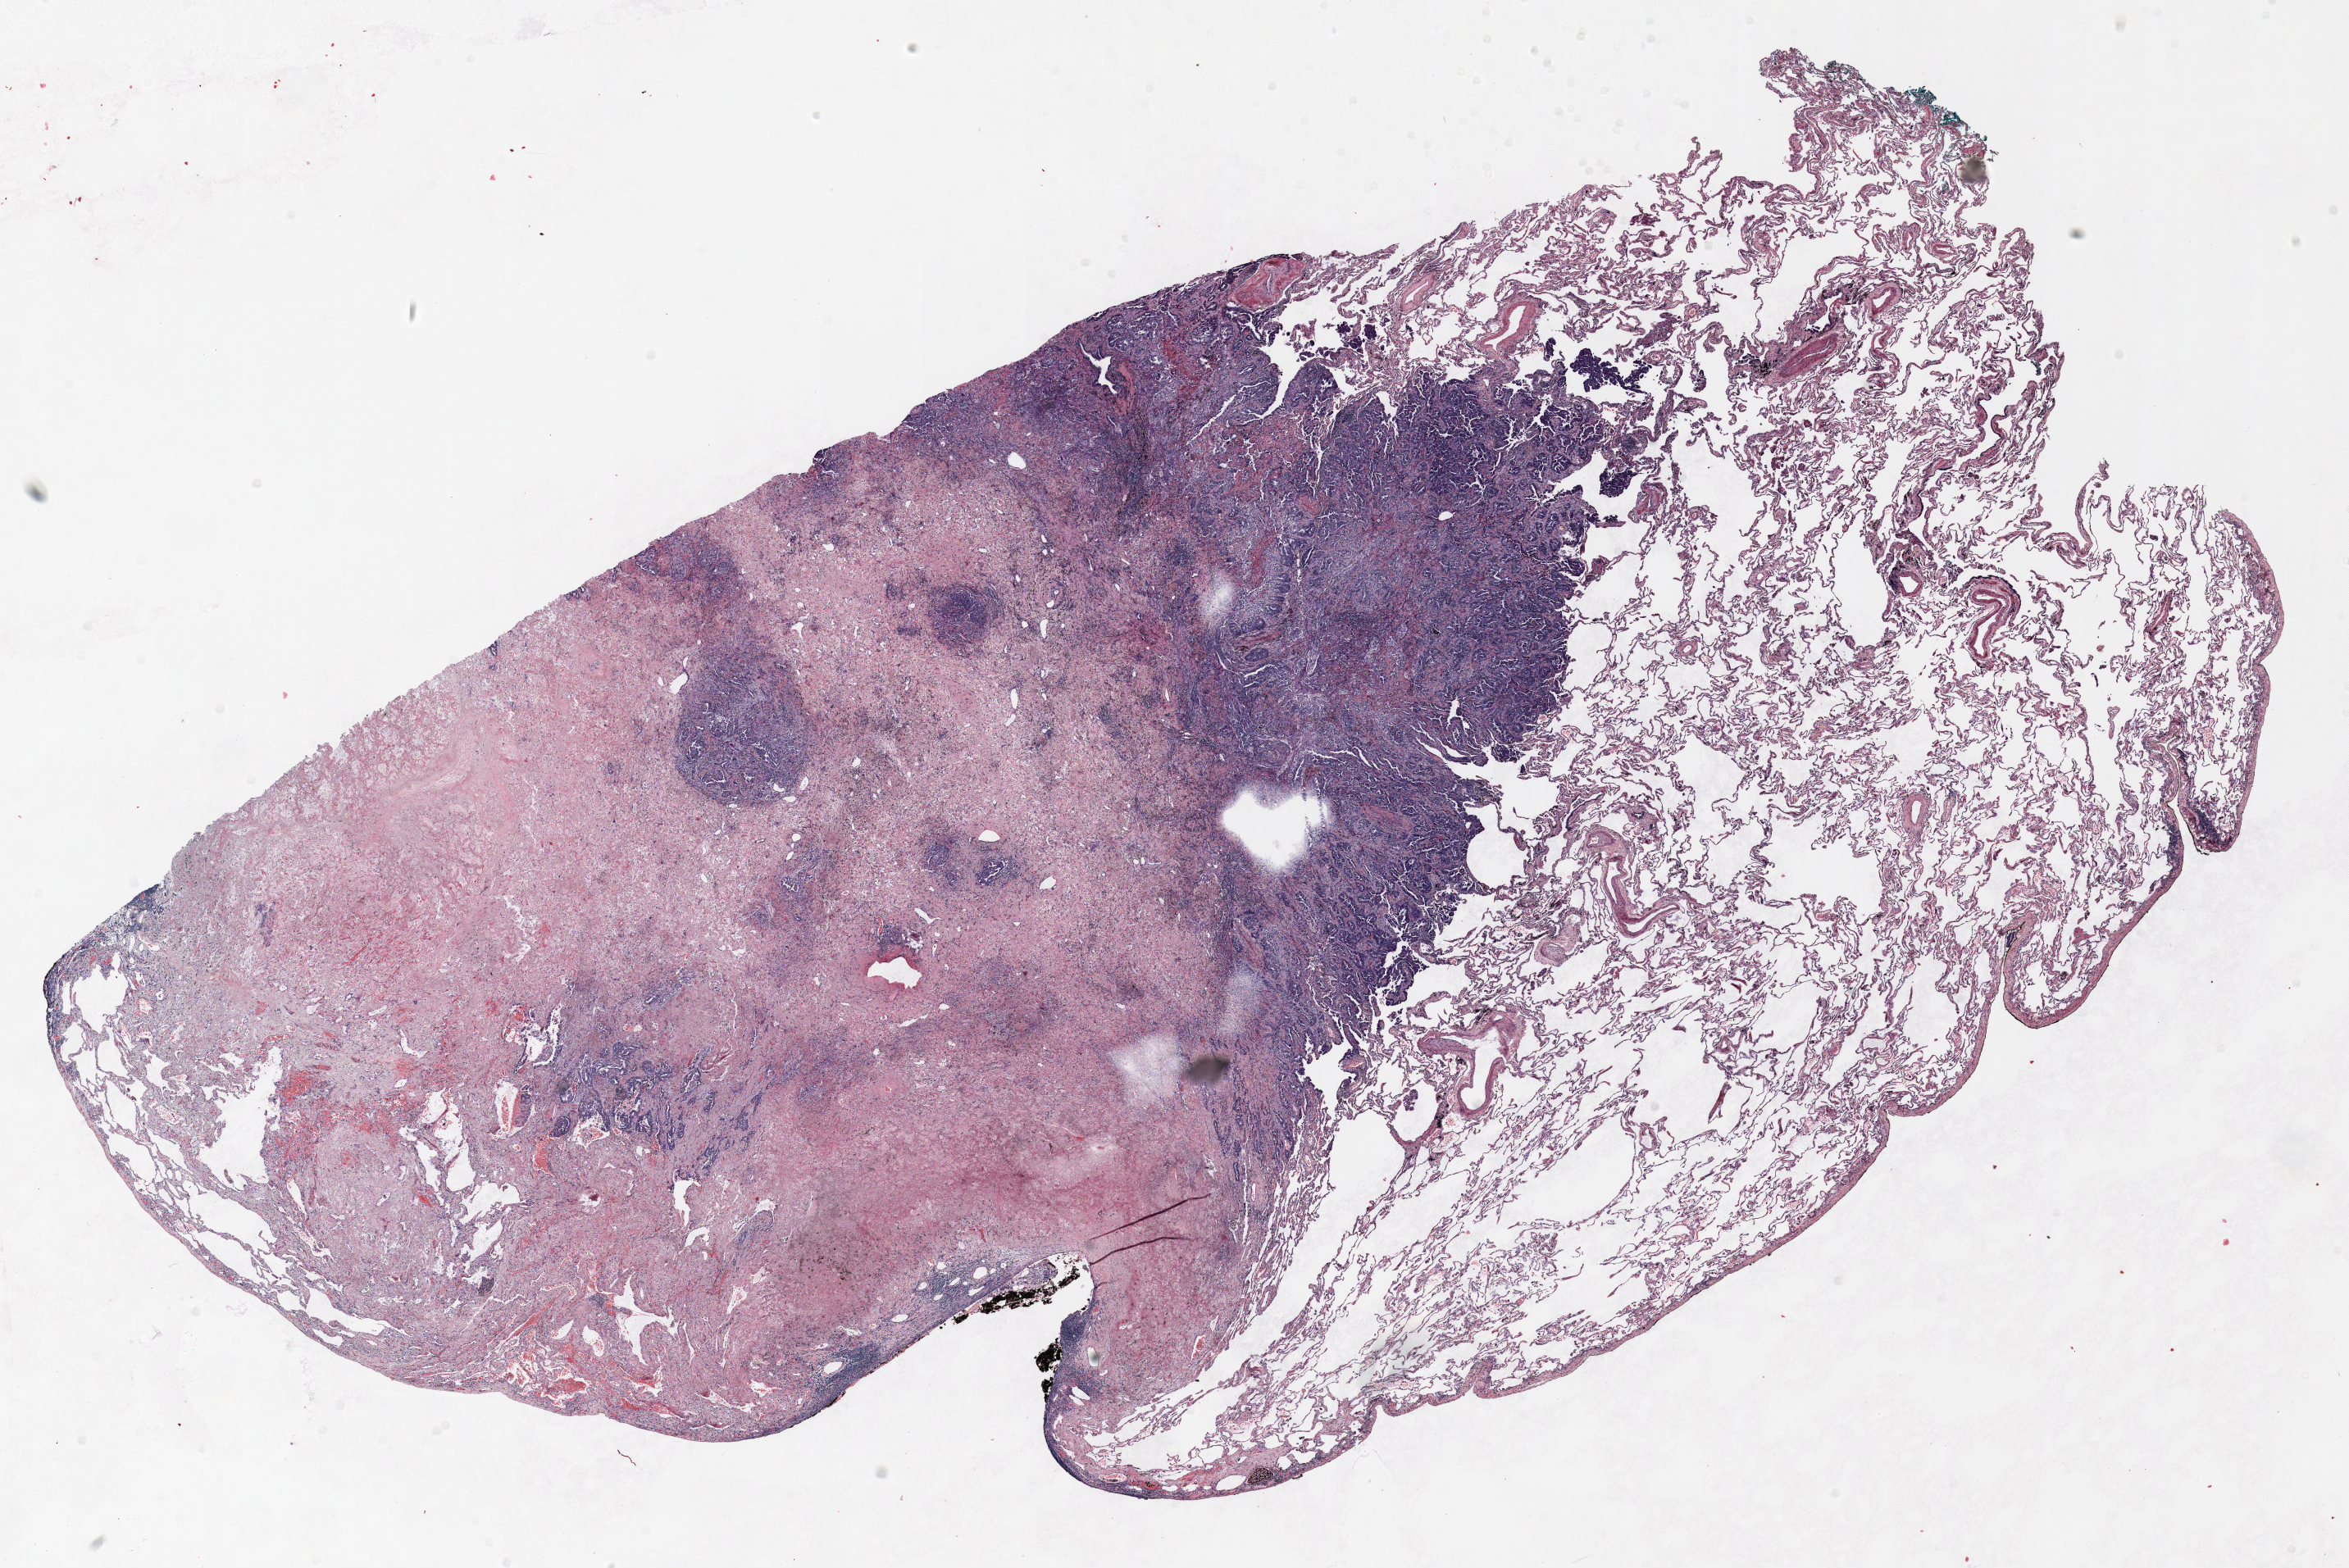
Whole-slide histology image, H&E-stained — whole scanned area (about 23.0 x 15.4 mm) shown as a low-resolution overview, formalin-fixed paraffin-embedded (FFPE) section, lung tissue. Female patient, aged 66 at enrolment. Former smoker at enrolment. Grade: poorly differentiated (G3).
Stage (AJCC 6th edition): IB. Primary tumour location (clinical record): left upper lobe. Tumour size (pathology): 40 mm. Participant's lung-cancer diagnosis: Adenocarcinoma, NOS (ICD-O-3 8140/3).